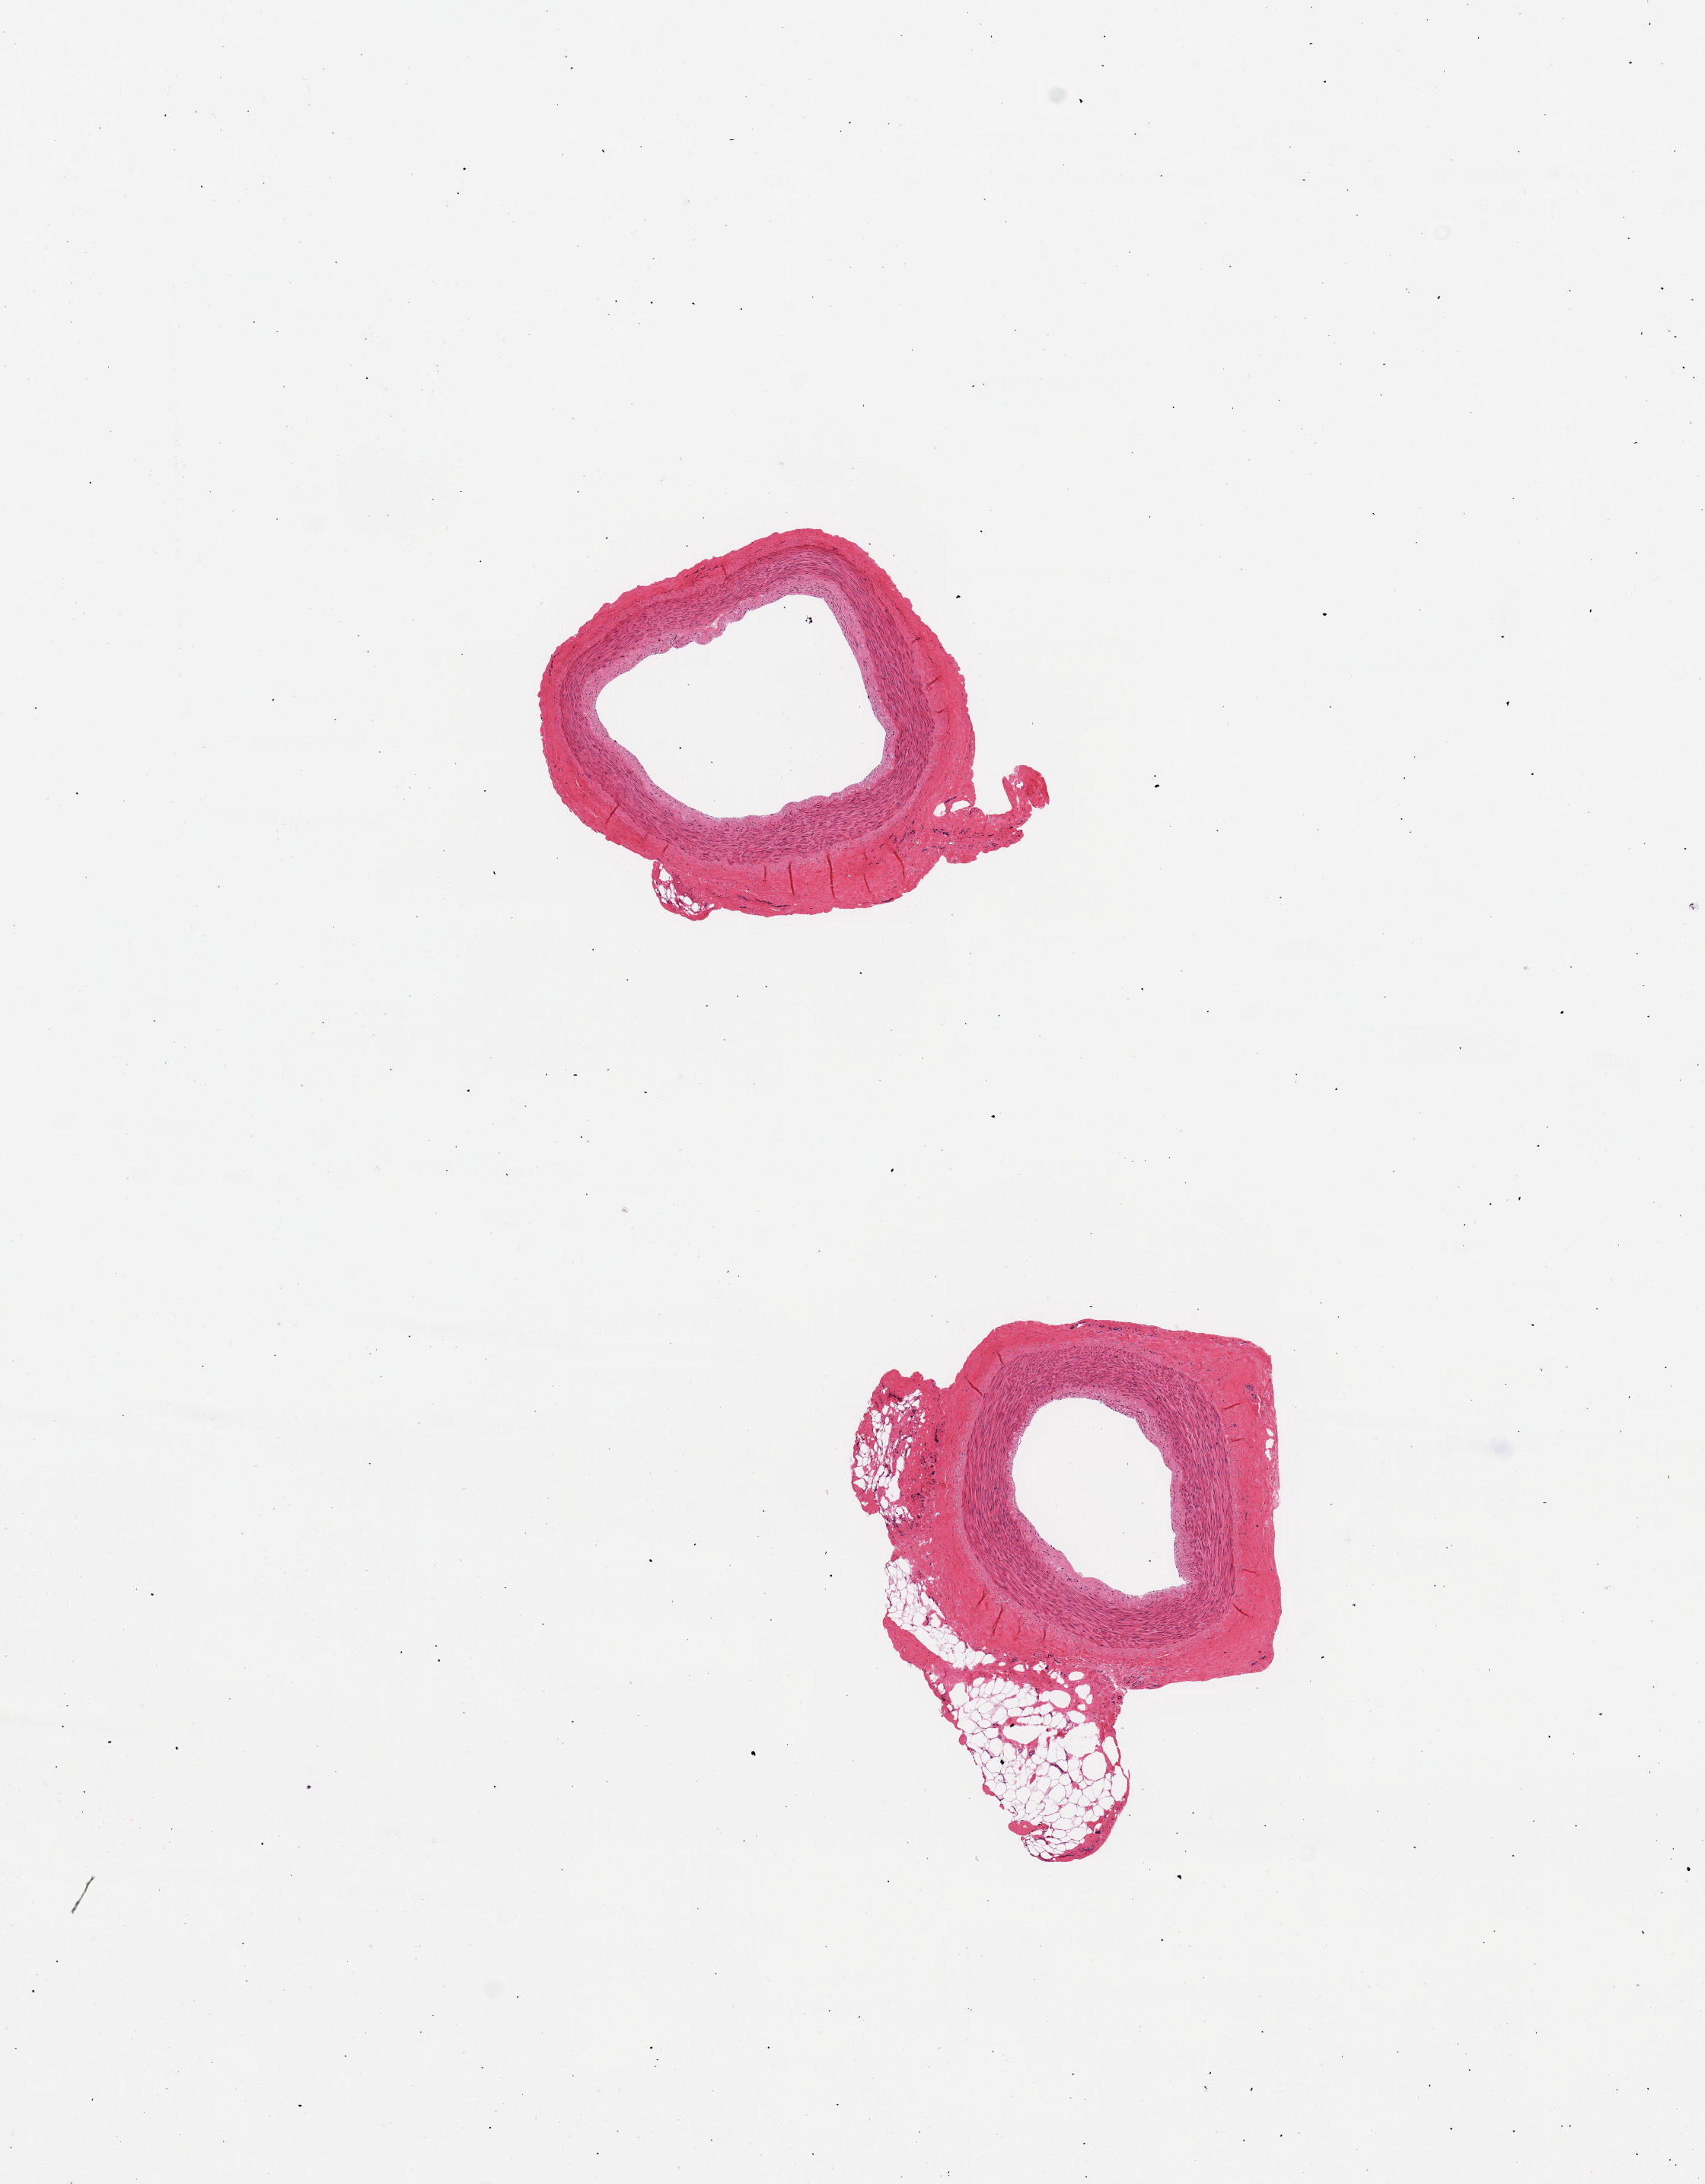
Hematoxylin and eosin (H&E) whole-slide image — whole scanned area (about 8.9 x 11.3 mm) shown as a low-resolution overview; PAXgene-fixed, paraffin-embedded tissue; sampled site (target tissue): tibial artery; tissue donor sample.
Reviewer comment on this tissue sample: 2 pieces; no lesions; external fat on 1 piece.